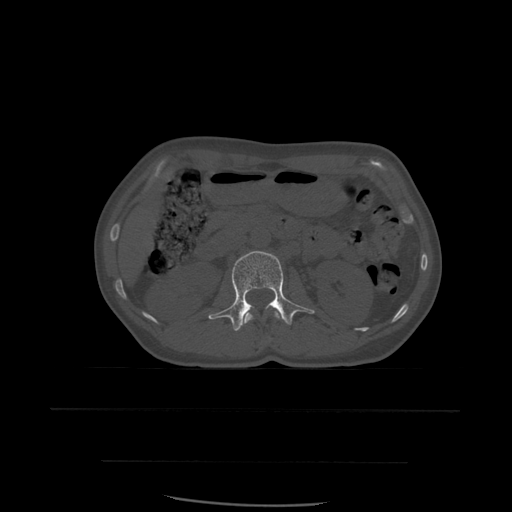
CT including the spine, one axial slice; slice 230 of 574 in the series (ordered by position); bone window (W 1800 / L 400 HU); 1.25 mm slice thickness; 512 × 512 image matrix, field of view 392 × 392 mm. Patient age 48 years. From the clinical record (not read from this slice): primary cancer: lung; vertebrae with lytic lesions (as recorded): T11.
Annotated regions visible in this slice (semi-automatically segmented with operator editing):
- L1 vertebra: bounding box (x1, y1, x2, y2) in pixels: (244, 311, 280, 325)
- L2 vertebra: (209, 251, 315, 332)